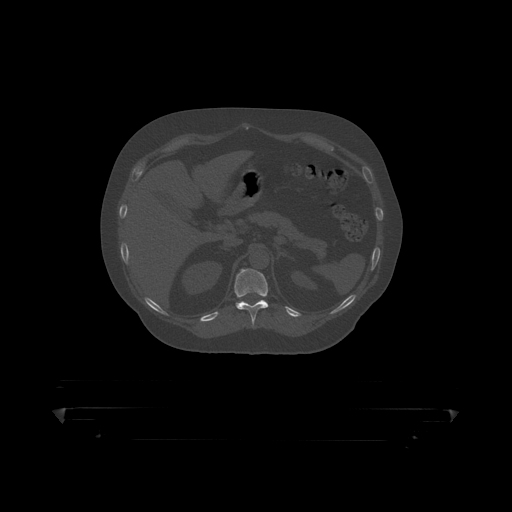
CT including the spine, one axial slice. Position 192 of 390 along the scan axis. Reconstruction kernel STANDARD. 120 kVp. Bone window (W 1800 / L 400 HU). 512 × 512 image matrix, field of view 650 × 650 mm. Patient: male, 60 years. From the clinical record (not read from this slice): primary cancer: prostate.
Annotated regions visible in this slice (semi-automatic segmentation, software-assisted and operator-edited):
- T11 vertebra: bounding box [x1, y1, x2, y2] px = [234, 269, 291, 319]